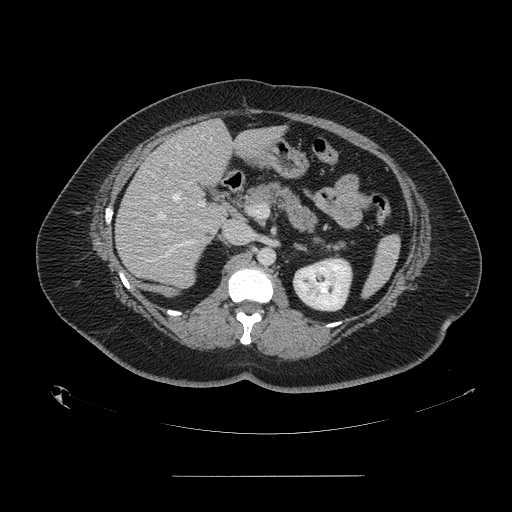
Contrast-enhanced abdominal CT, one axial slice; position 81 of 164 along the scan axis; 120 kVp; intravenous contrast given; soft-tissue window (W 400 / L 40 HU); 2.5 mm slice thickness; 512 × 512 image matrix. Female patient, age 52 years. From the clinical record (not read from this slice): diagnosis: colorectal cancer liver metastases, imaged before liver resection; multiple liver metastases: yes; largest metastasis: 3.5 cm.
Annotated regions visible in this slice (outlined manually by an expert reader):
- hepatic veins: bounding box [x1, y1, x2, y2] px = [152, 135, 203, 219]
- liver: [116, 121, 280, 287]
- planned liver remnant (the part of the liver to remain after resection): [177, 121, 280, 183]
- portal vein (with intrahepatic branches): [162, 179, 205, 237]
- liver metastasis: [204, 230, 214, 238]